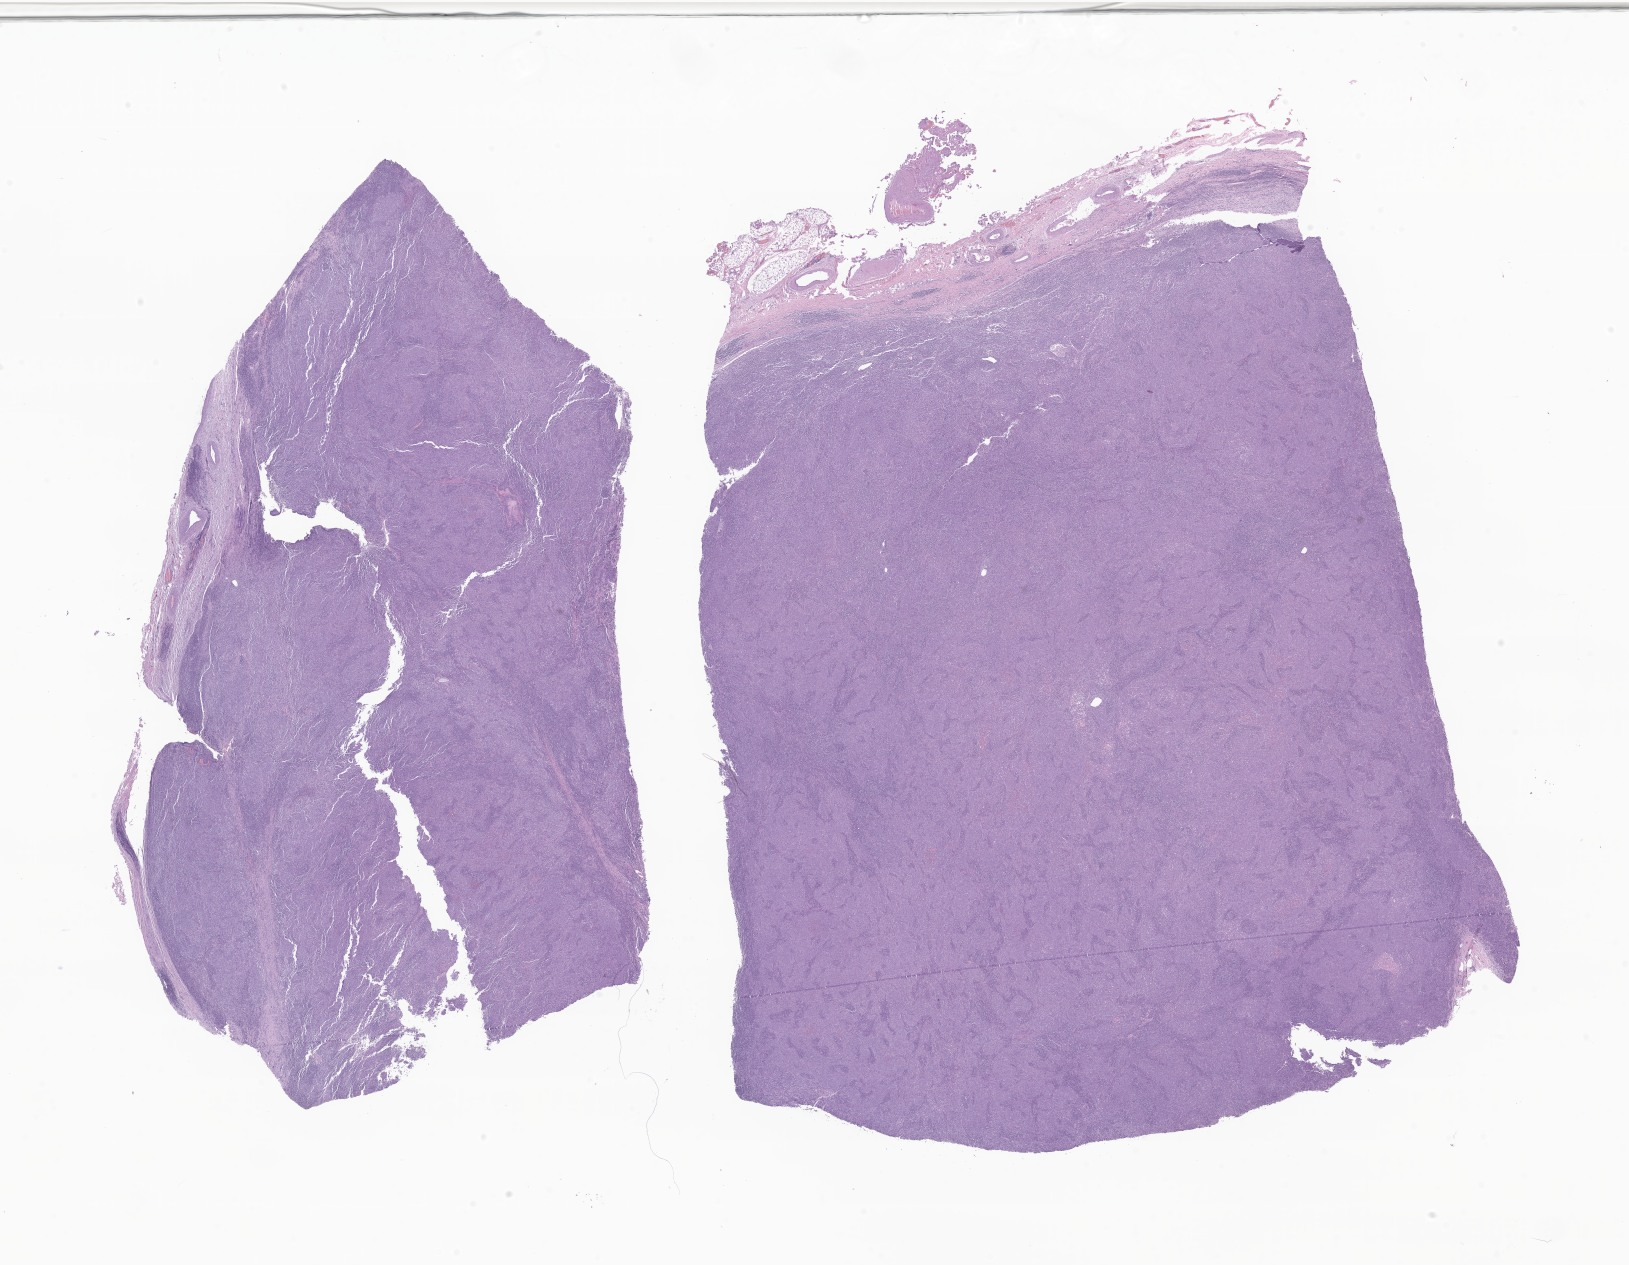
Whole-slide image, hematoxylin and eosin (H&E) stain of tumor tissue from the head and neck, low-resolution overview of the scanned area, about 27.5 x 21.3 mm. Formalin-fixed paraffin-embedded section. Male patient, age 202 months.
Recorded diagnosis: Carcinoma, NOS. Tissue or organ of origin (case record): head, face or neck.